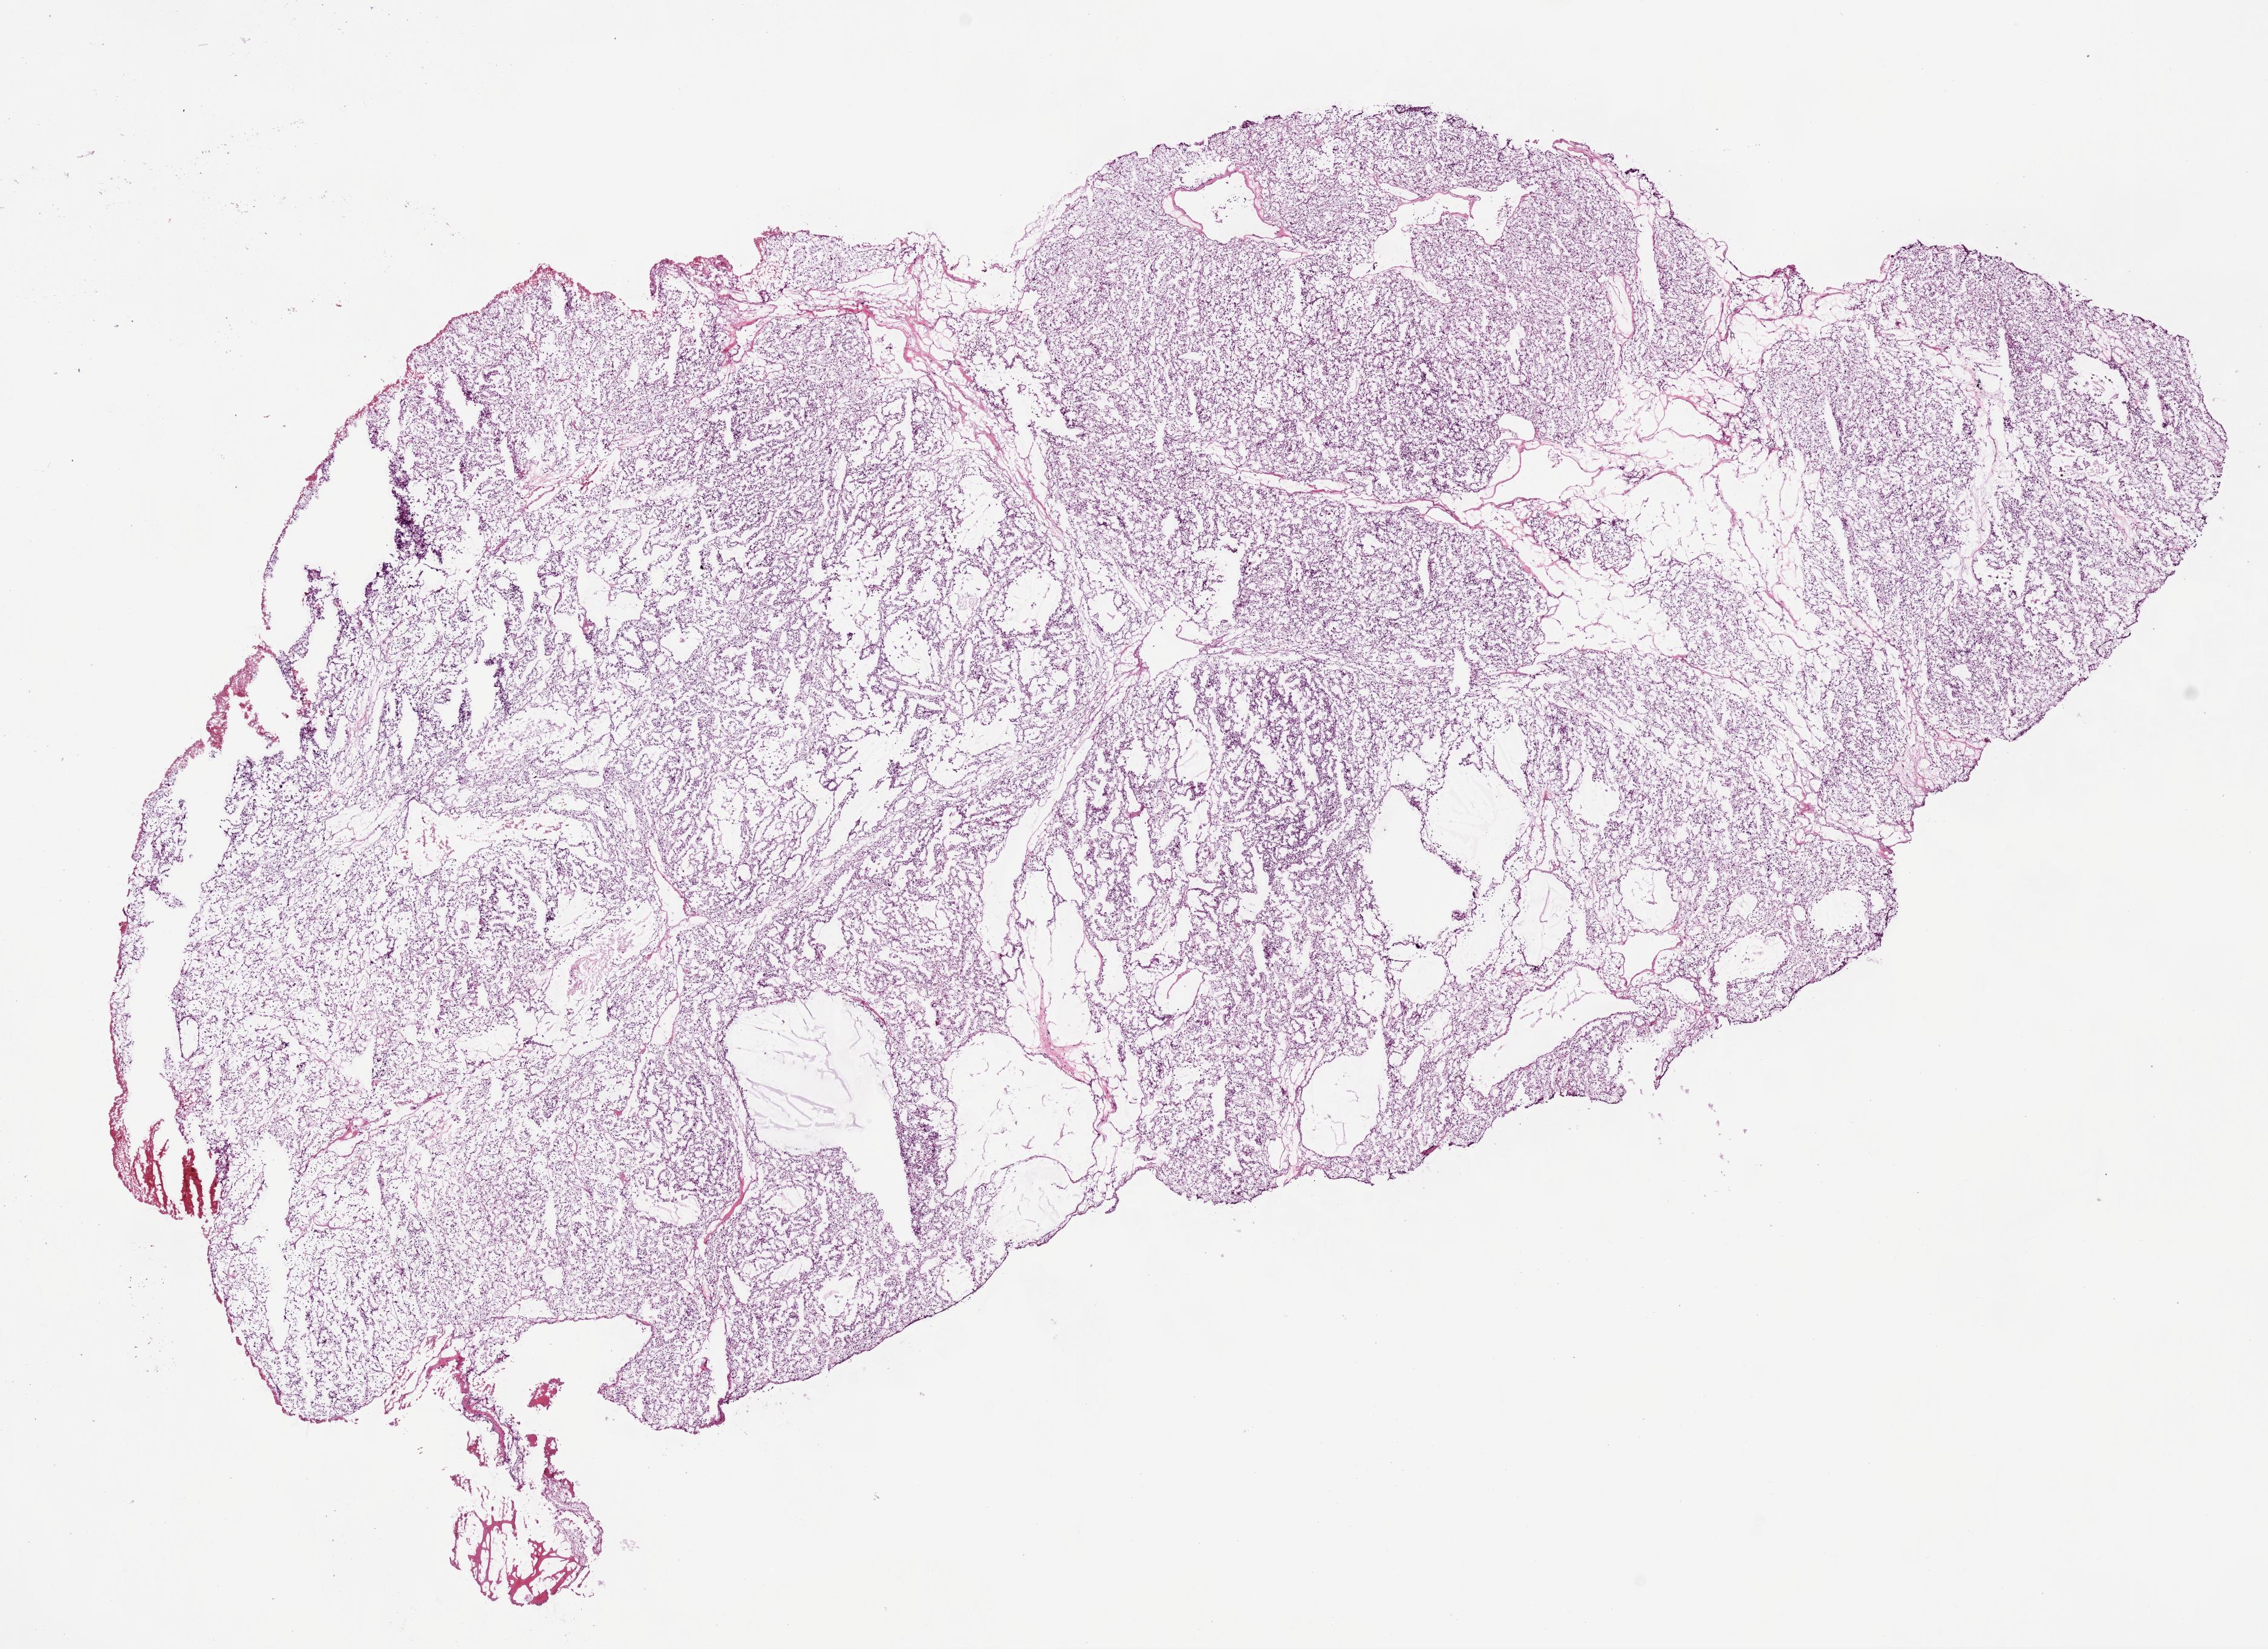
Whole-slide histology image, H&E — a low-resolution overview of the entire scanned area, about 15.0 x 10.9 mm (from a 20x scan); frozen section; sample: primary tumour, kidney. Male patient; age at initial diagnosis 67 years. Histologic grade: G2 (moderately differentiated). Composition of this section per pathologist review: tumour cells 95%, tumour nuclei 90%, normal cells 0%, stromal cells 5%, necrosis 0%. Inflammatory infiltration, as recorded: lymphocyte infiltration 2%, monocyte infiltration 0%, neutrophil infiltration 0%.
AJCC pathologic stage: II (6th edition). Laterality: left. Histologic diagnosis: Clear cell adenocarcinoma, NOS.